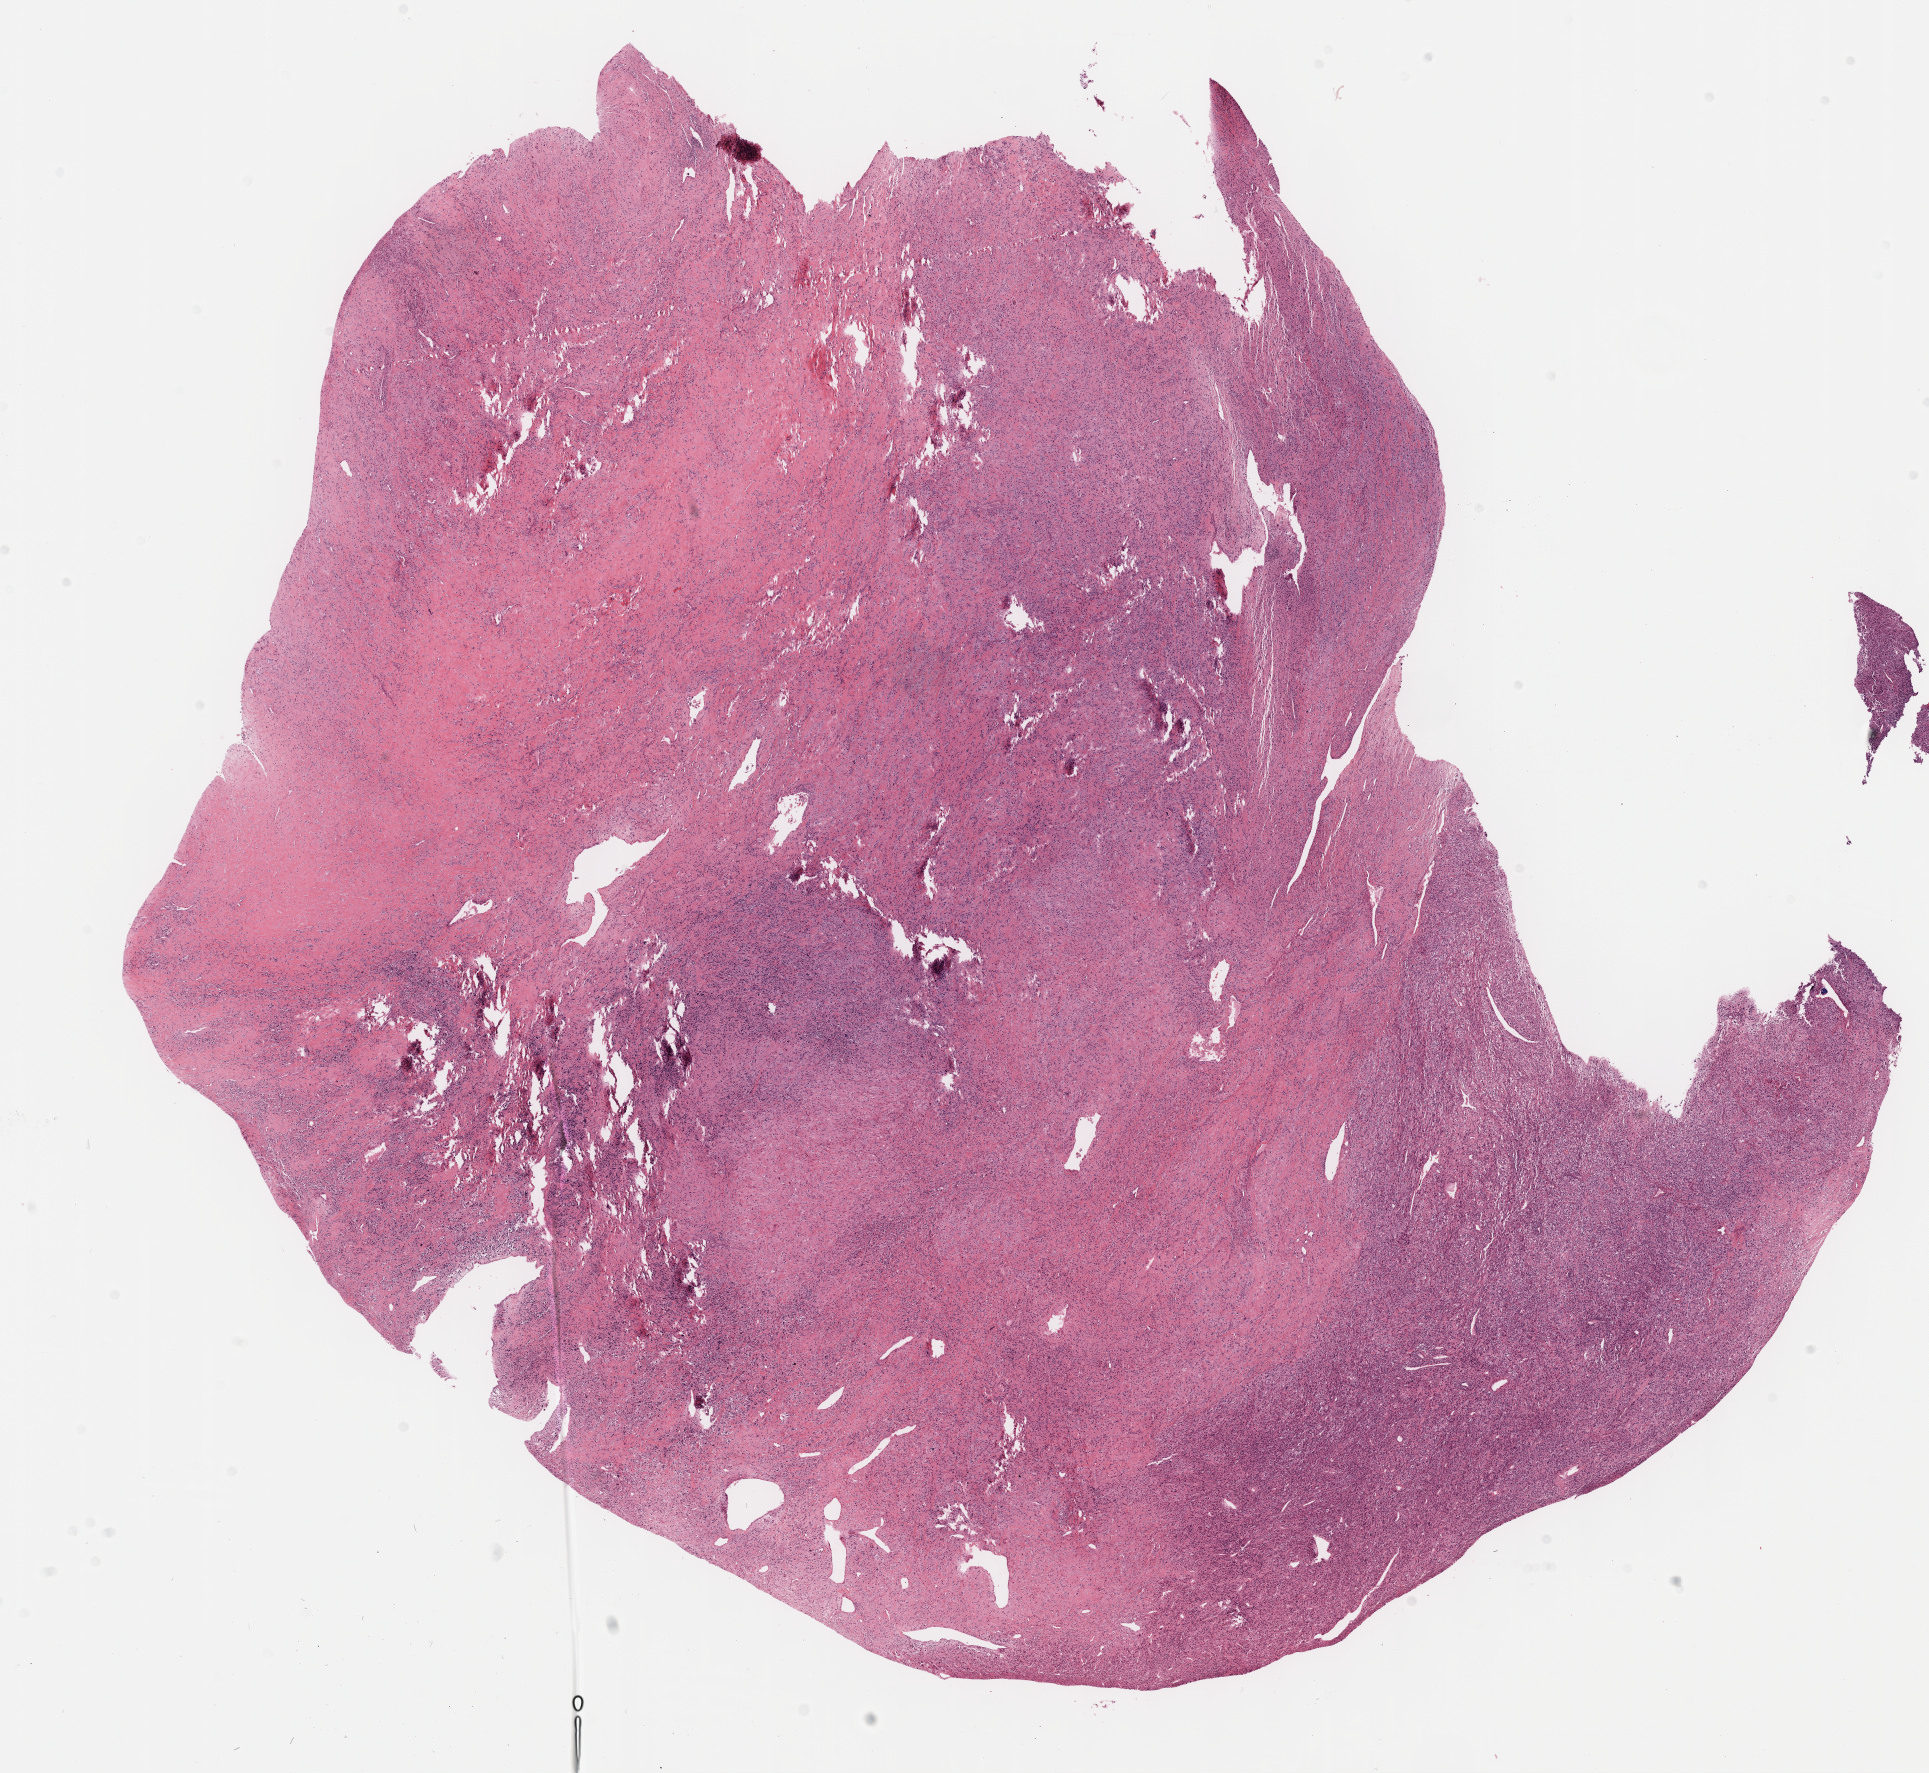
Digitized H&E-stained tissue section (whole slide) — low-resolution overview of the scanned area, about 15.6 x 14.3 mm (from a 40x scan), formalin-fixed paraffin-embedded (FFPE) diagnostic section, primary tumour sample from the connective, subcutaneous and other soft tissues. Male, age 58 years at initial diagnosis.
Pathologic diagnosis: Malignant fibrous histiocytoma (connective, subcutaneous and other soft tissues of lower limb and hip).